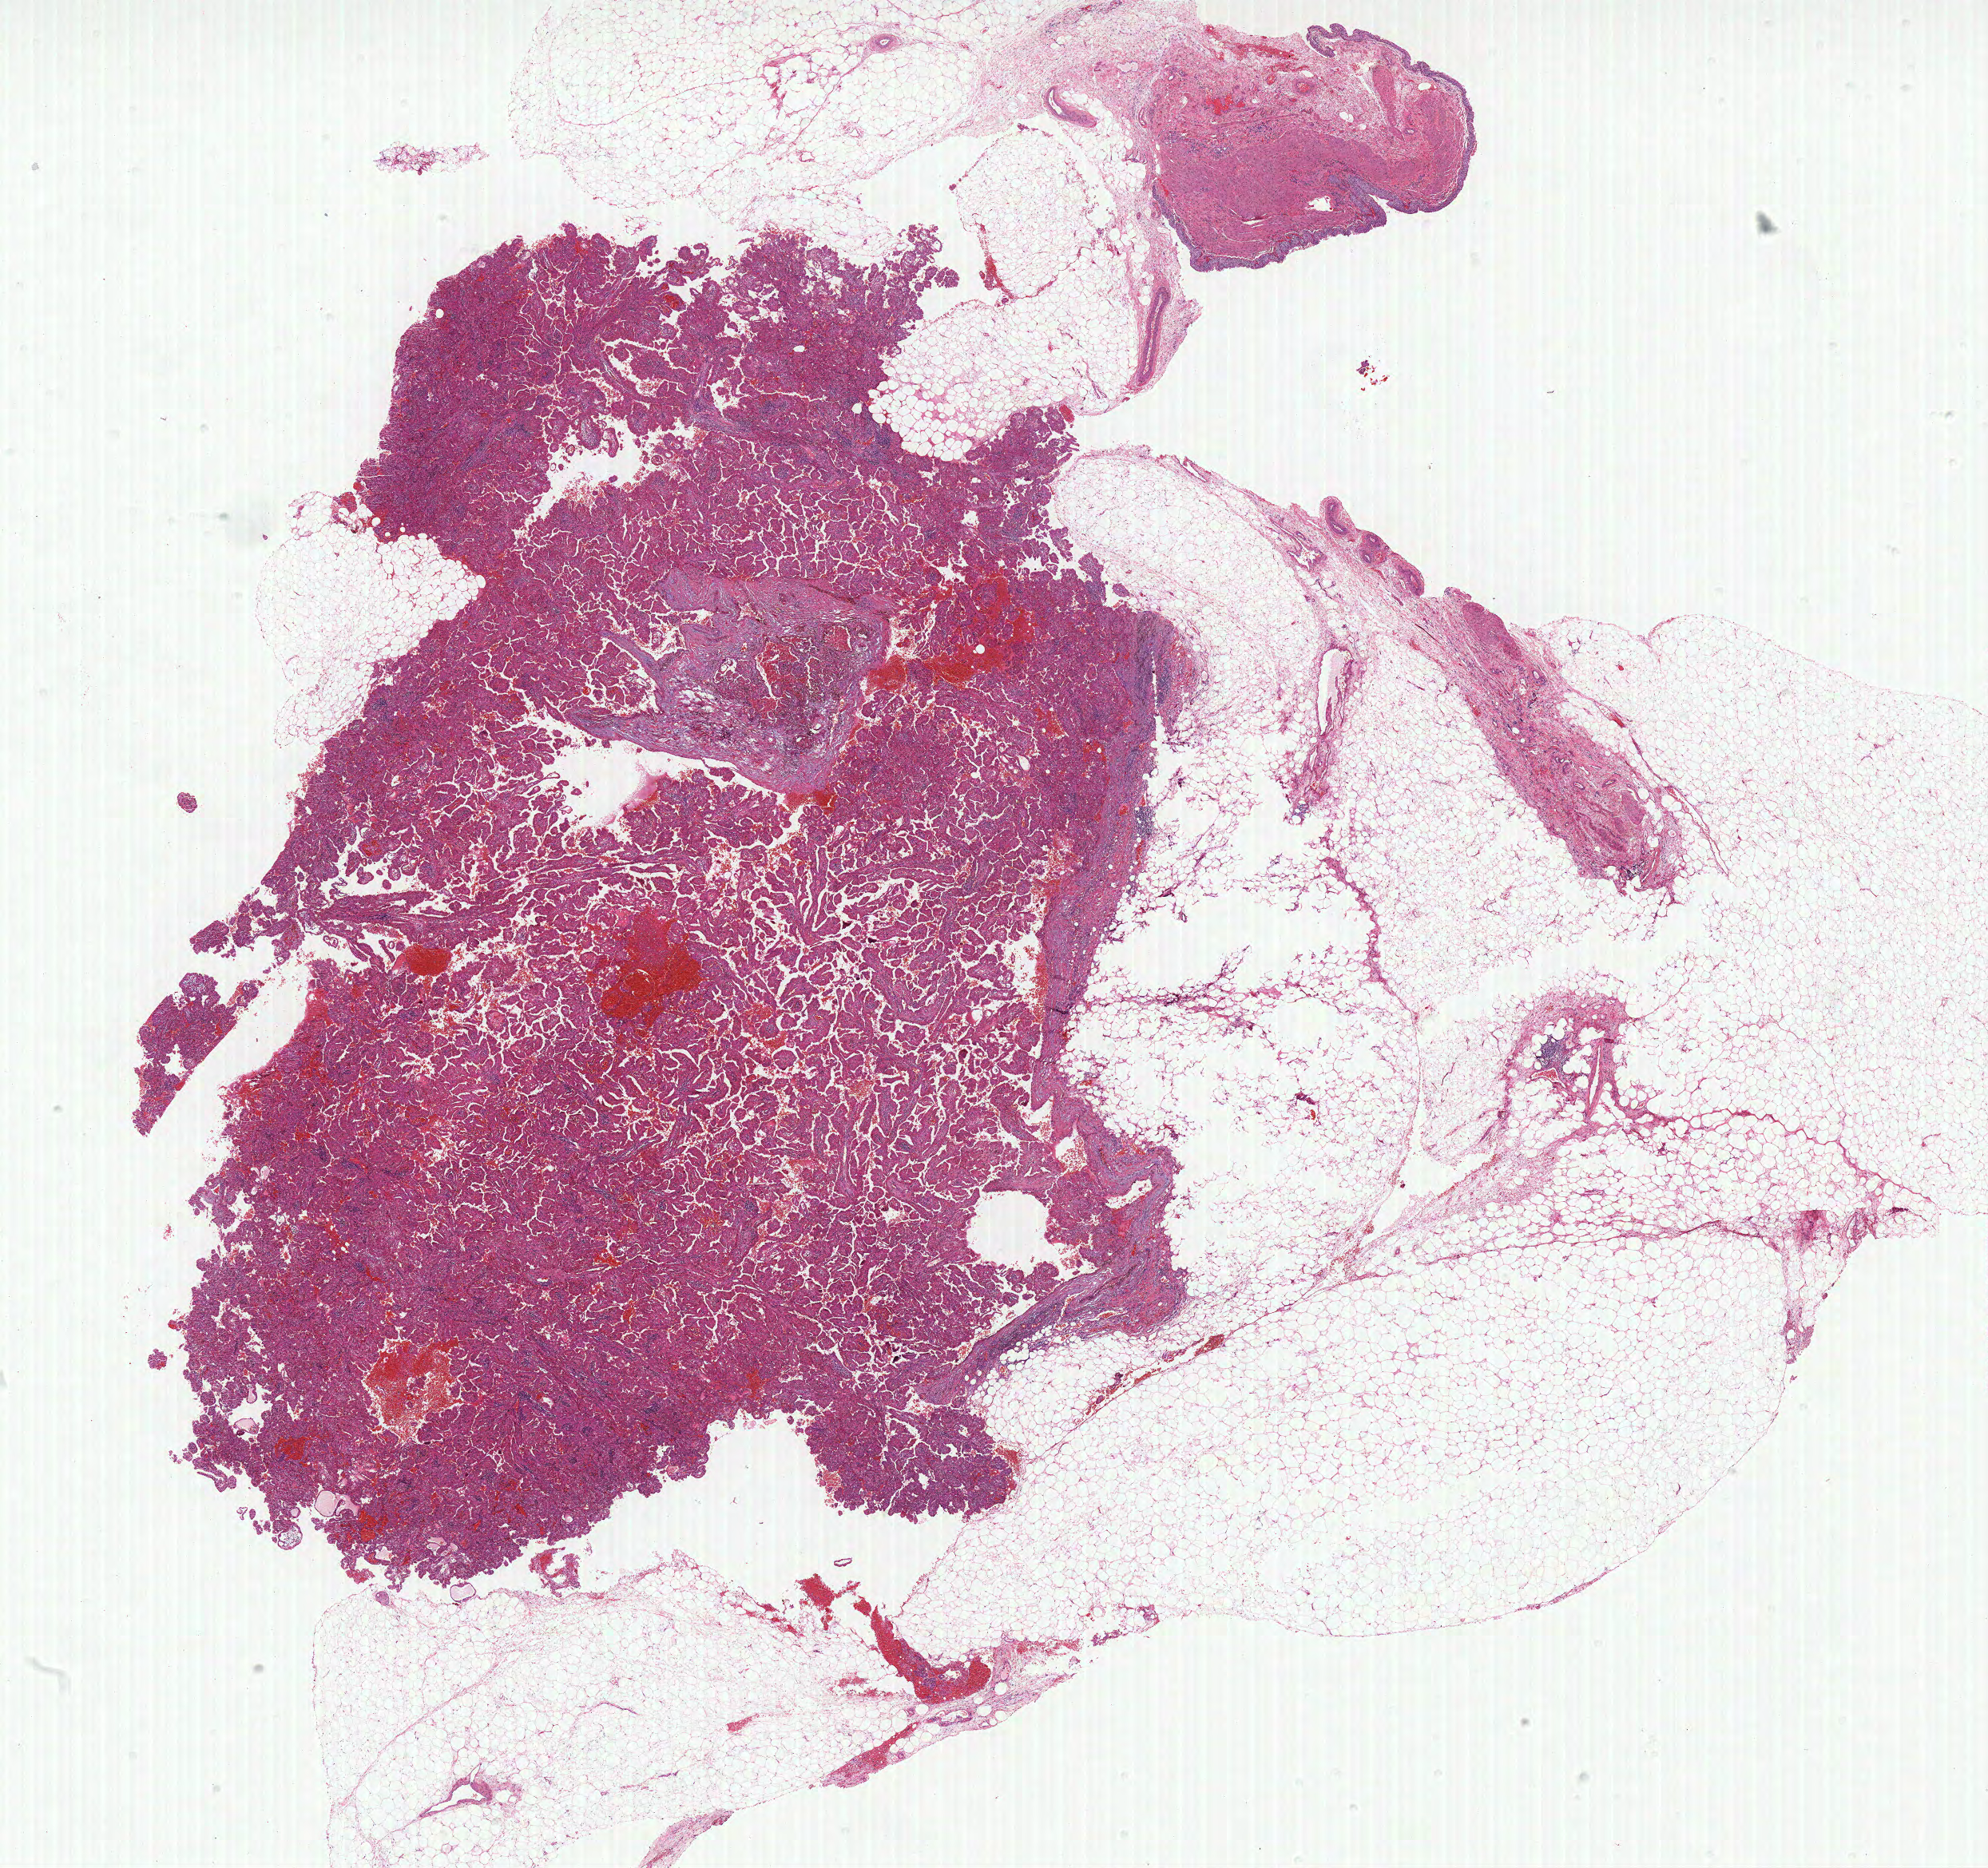
H&E-stained whole-slide image — whole scanned area (about 19.9 x 18.7 mm) shown as a low-resolution overview. Formalin-fixed paraffin-embedded (FFPE) diagnostic section. Sample: primary tumour, kidney. Male patient; age at initial diagnosis 79 years.
Diagnosis: Papillary adenocarcinoma, NOS.